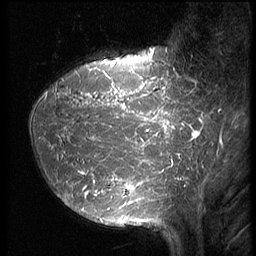
Breast MRI (dynamic contrast-enhanced), one sagittal slice. Slice 17 of 64 in the series (ordered by position). 3 images stored at this slice position (order not interpretable as contrast timing). 1.5 T. TE 4.2 ms, TR 9 ms. 2.5 mm slice thickness. 256 × 256 image matrix. Female patient, age 39 years. From the clinical record (not read from this slice): setting: breast cancer imaged before/during neoadjuvant chemotherapy; receptor status: HER2-positive.
Annotated regions visible in this slice (semi-automatic segmentation, software-assisted and operator-edited):
- analysis volume of interest (the breast-tissue region the enhancement analysis was run in; not a lesion): box from (x=29, y=47) to (x=210, y=239) px
- tumour enhancement mask (voxels above the 140 % enhancement threshold inside the analysis volume of interest): (x=65, y=49)–(x=209, y=210)